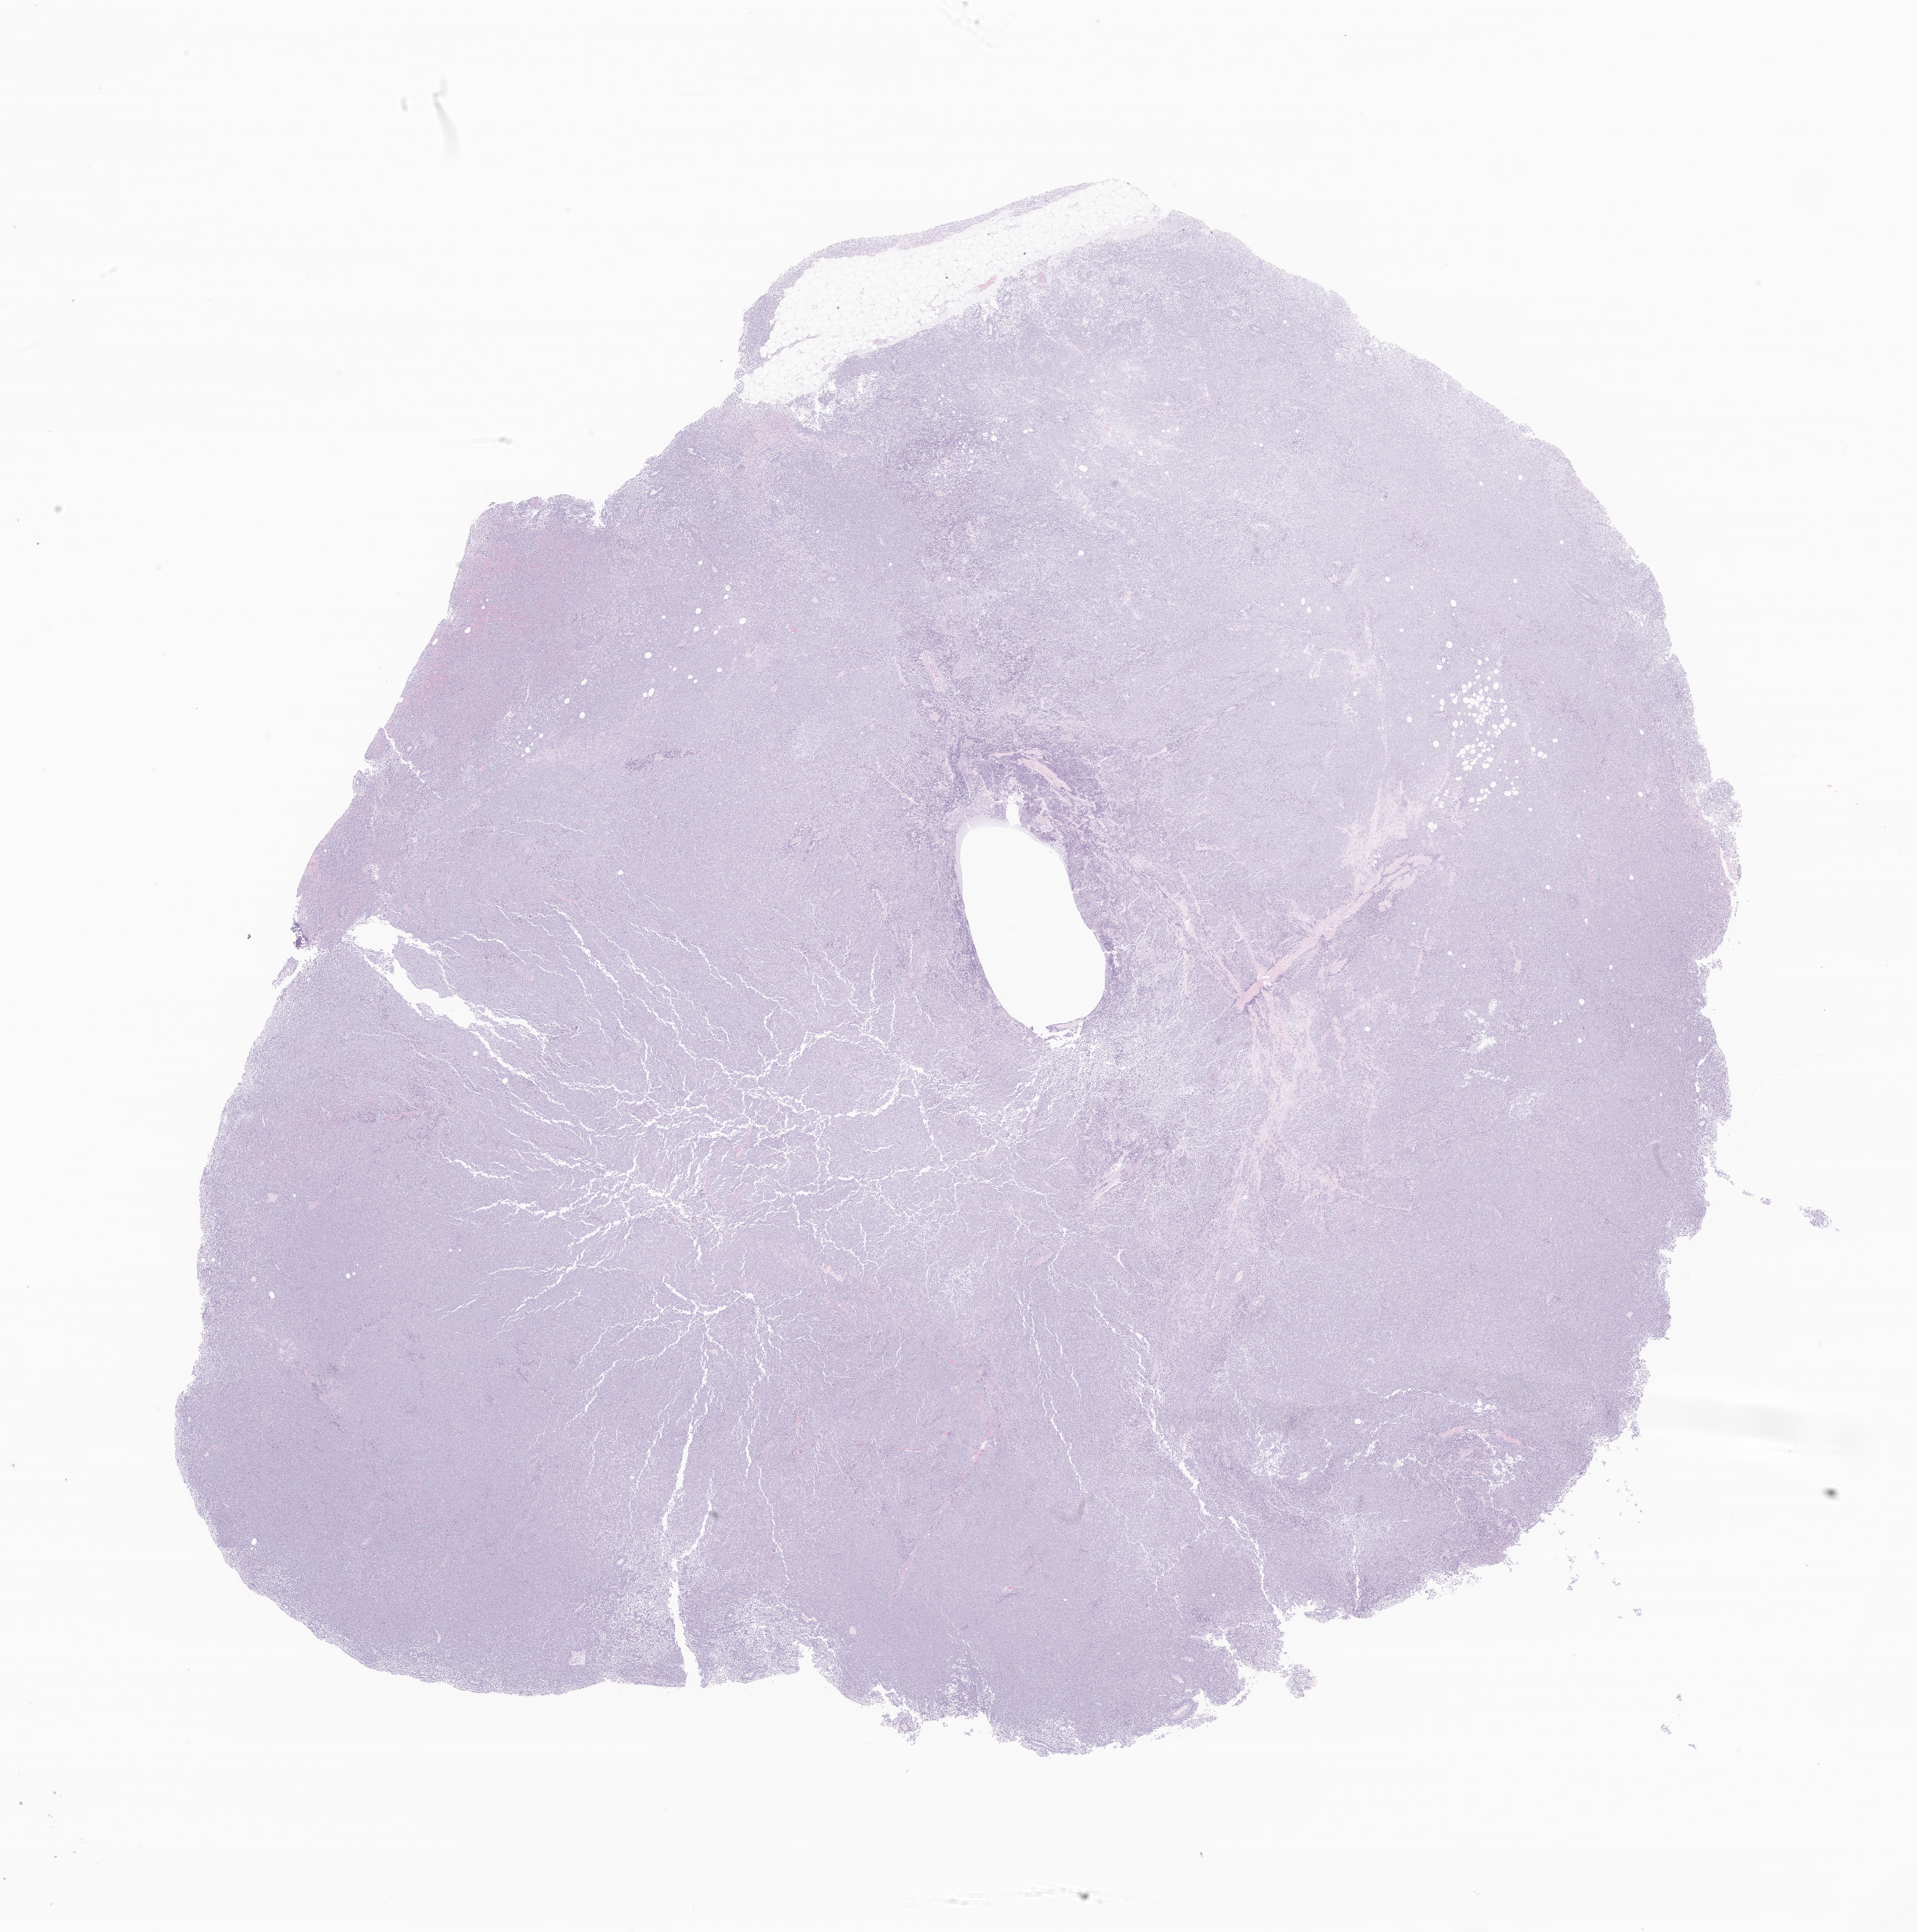
Haematoxylin and eosin whole-slide image of tumor tissue from the soft tissue of thorax, whole scanned area (about 21.1 x 21.3 mm) shown as a low-resolution overview. Formalin-fixed paraffin-embedded section. Patient: female, age 143 months (11 years 11 months).
Diagnosis (ICD-O-3 morphology term): Malignant melanoma, NOS.